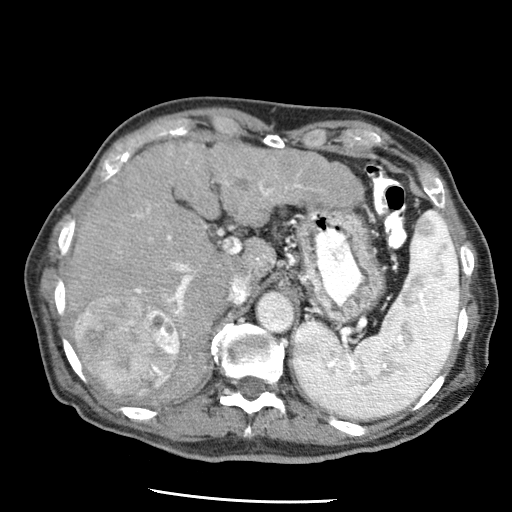
Contrast-enhanced abdominal CT (liver protocol), one axial slice; position 39 of 79 along the scan axis; 120 kVp; soft-tissue window (W 400 / L 40 HU); 512 × 512 image matrix, field of view 320 × 320 mm. Case-level facts recorded for this patient, not image findings: diagnosis: hepatocellular carcinoma (patient treated with transarterial chemoembolisation; whether this scan precedes or follows treatment is not stated here); TNM stage (as recorded): Stage-IIIA; Child-Pugh class: A; tumour differentiation: moderately differentiated.
Structures marked on this image (semi-automatically segmented with operator editing):
- liver parenchyma outside the tumour (the mass and vessels are separate outlines, so this box may not span the whole liver): bounding box [x1, y1, x2, y2] px = [64, 142, 344, 404]
- mass: [74, 293, 179, 397]
- liver vessels: [133, 162, 302, 336]